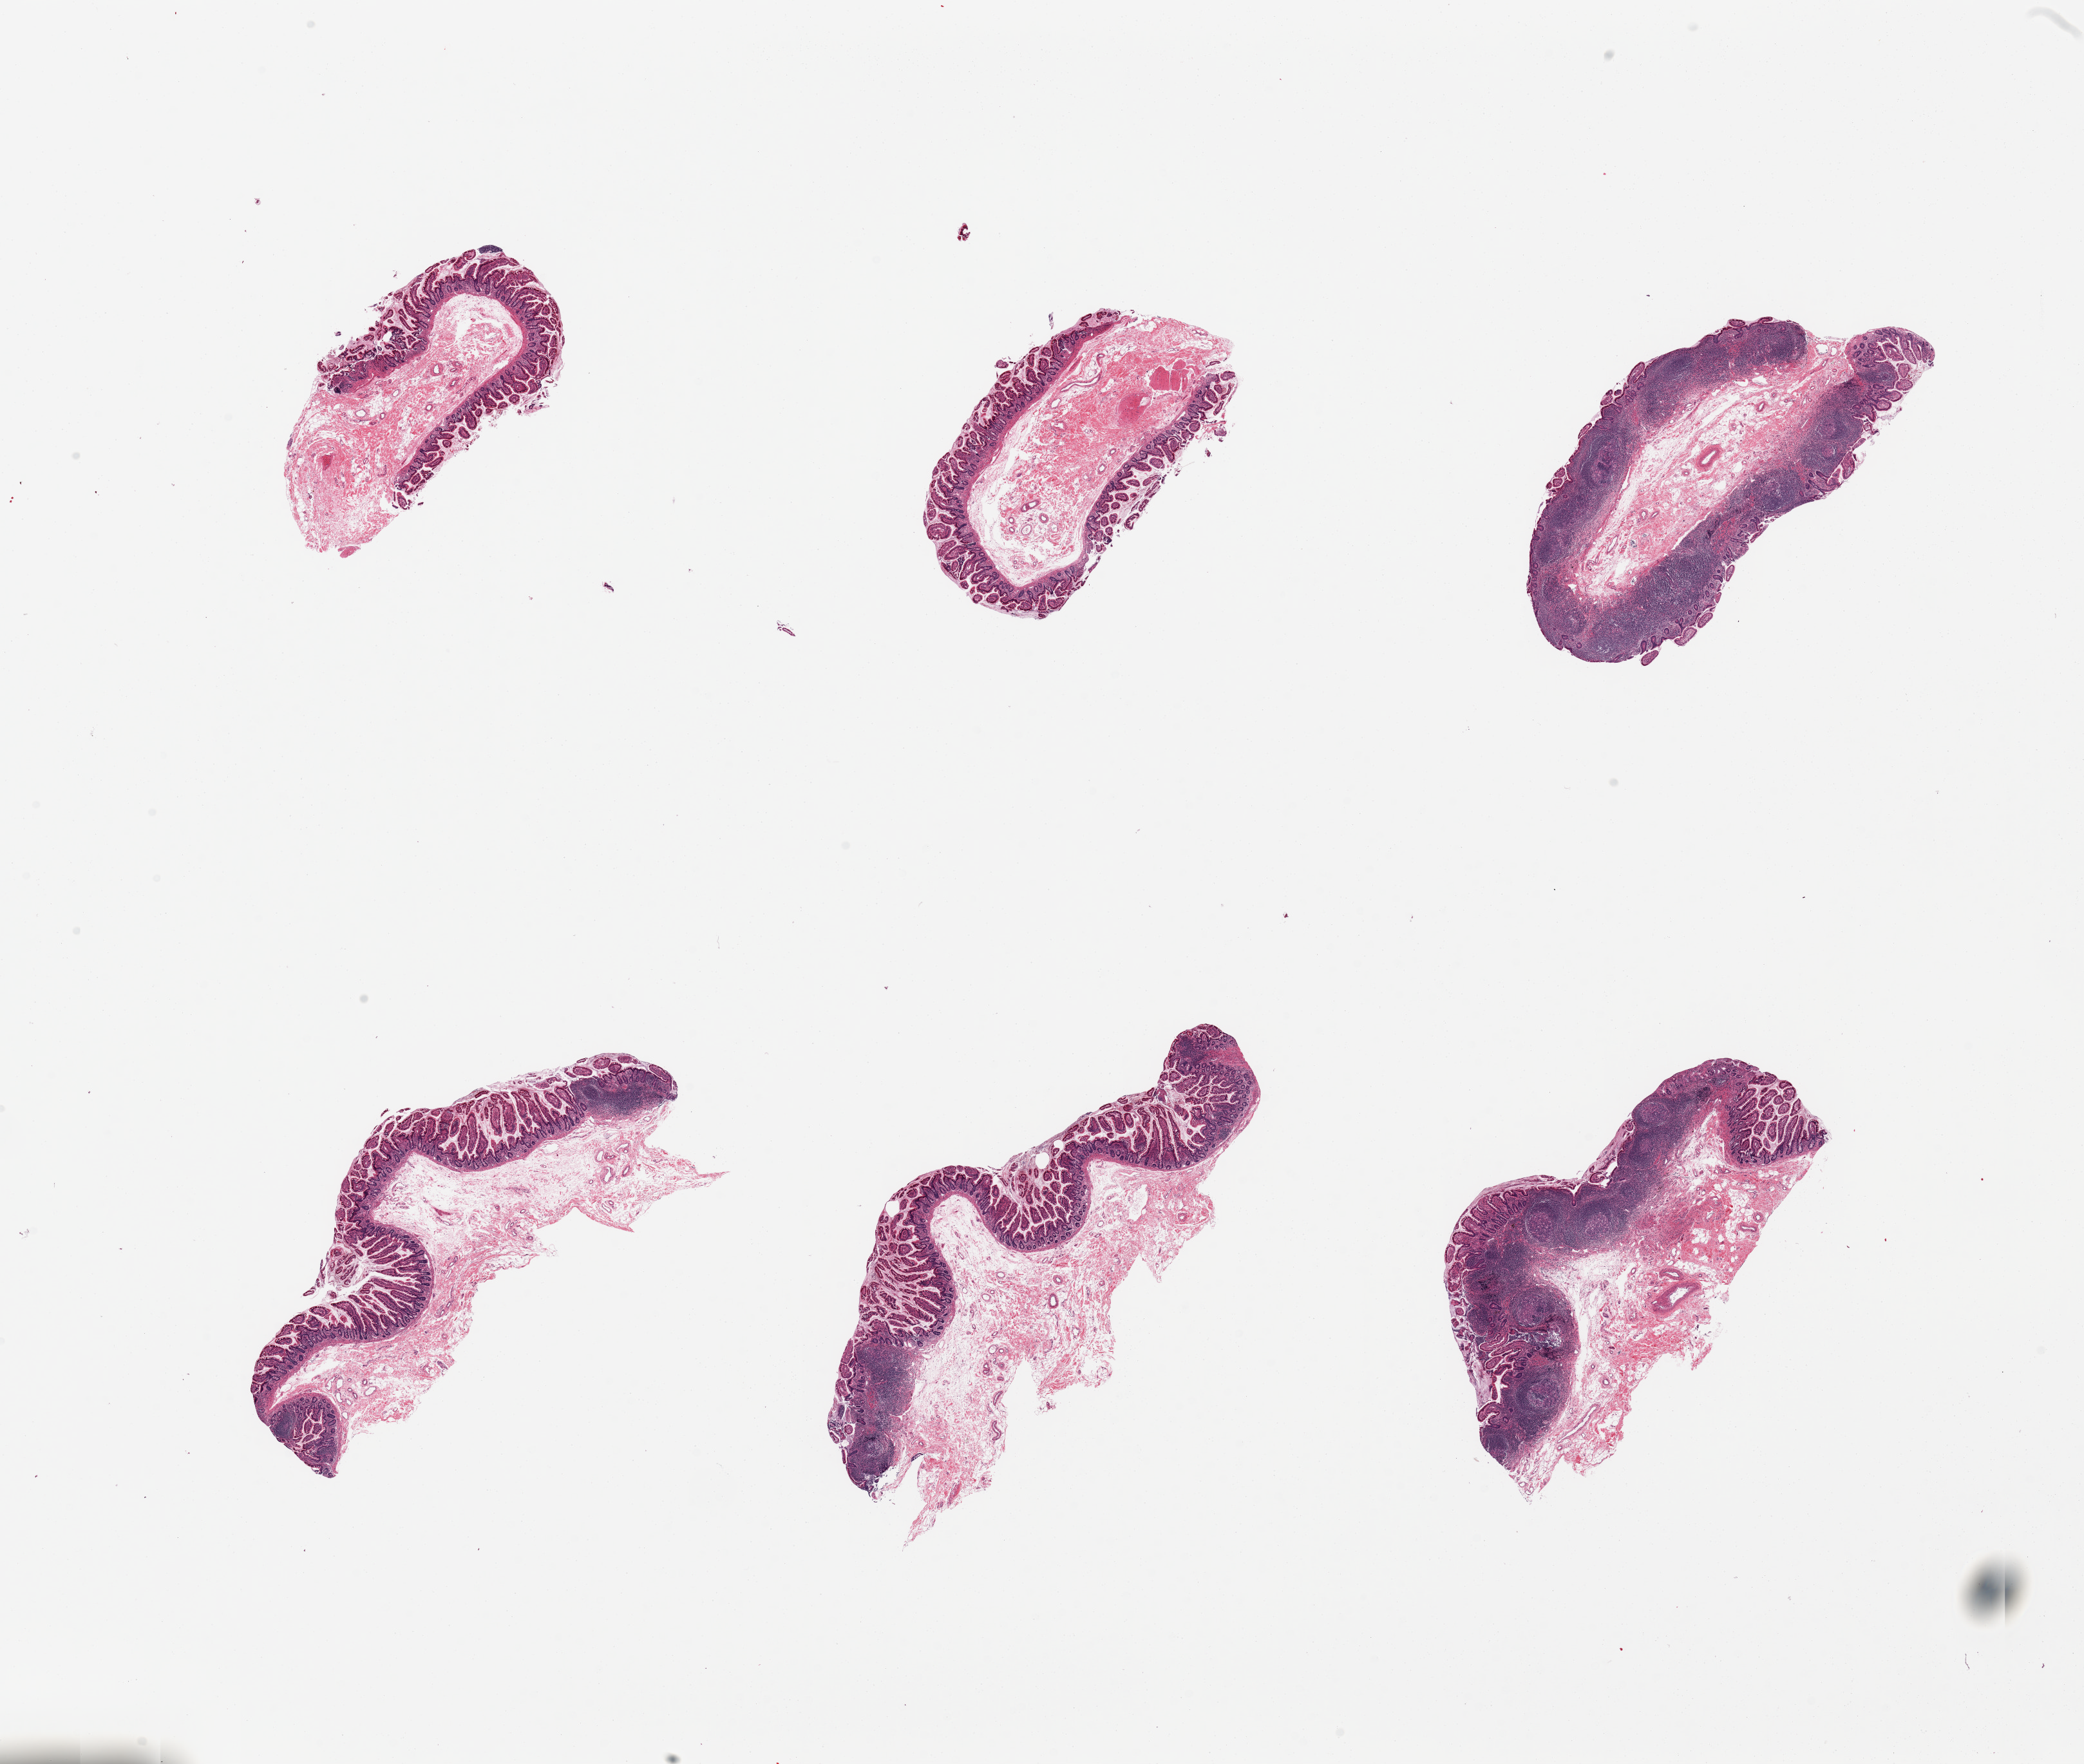
Digitized H&E-stained section, brightfield — whole scanned area (about 25.6 x 21.7 mm) shown as a low-resolution overview. PAXgene-fixed, paraffin-embedded tissue. Section of ileum (target tissue). Donor tissue sample.
Pathologist's review note for this sample: 6 pieces; 2 have extensive lymphoid areas; 2 have focal lymphoid areas; 2 have no lymphoid tissue.